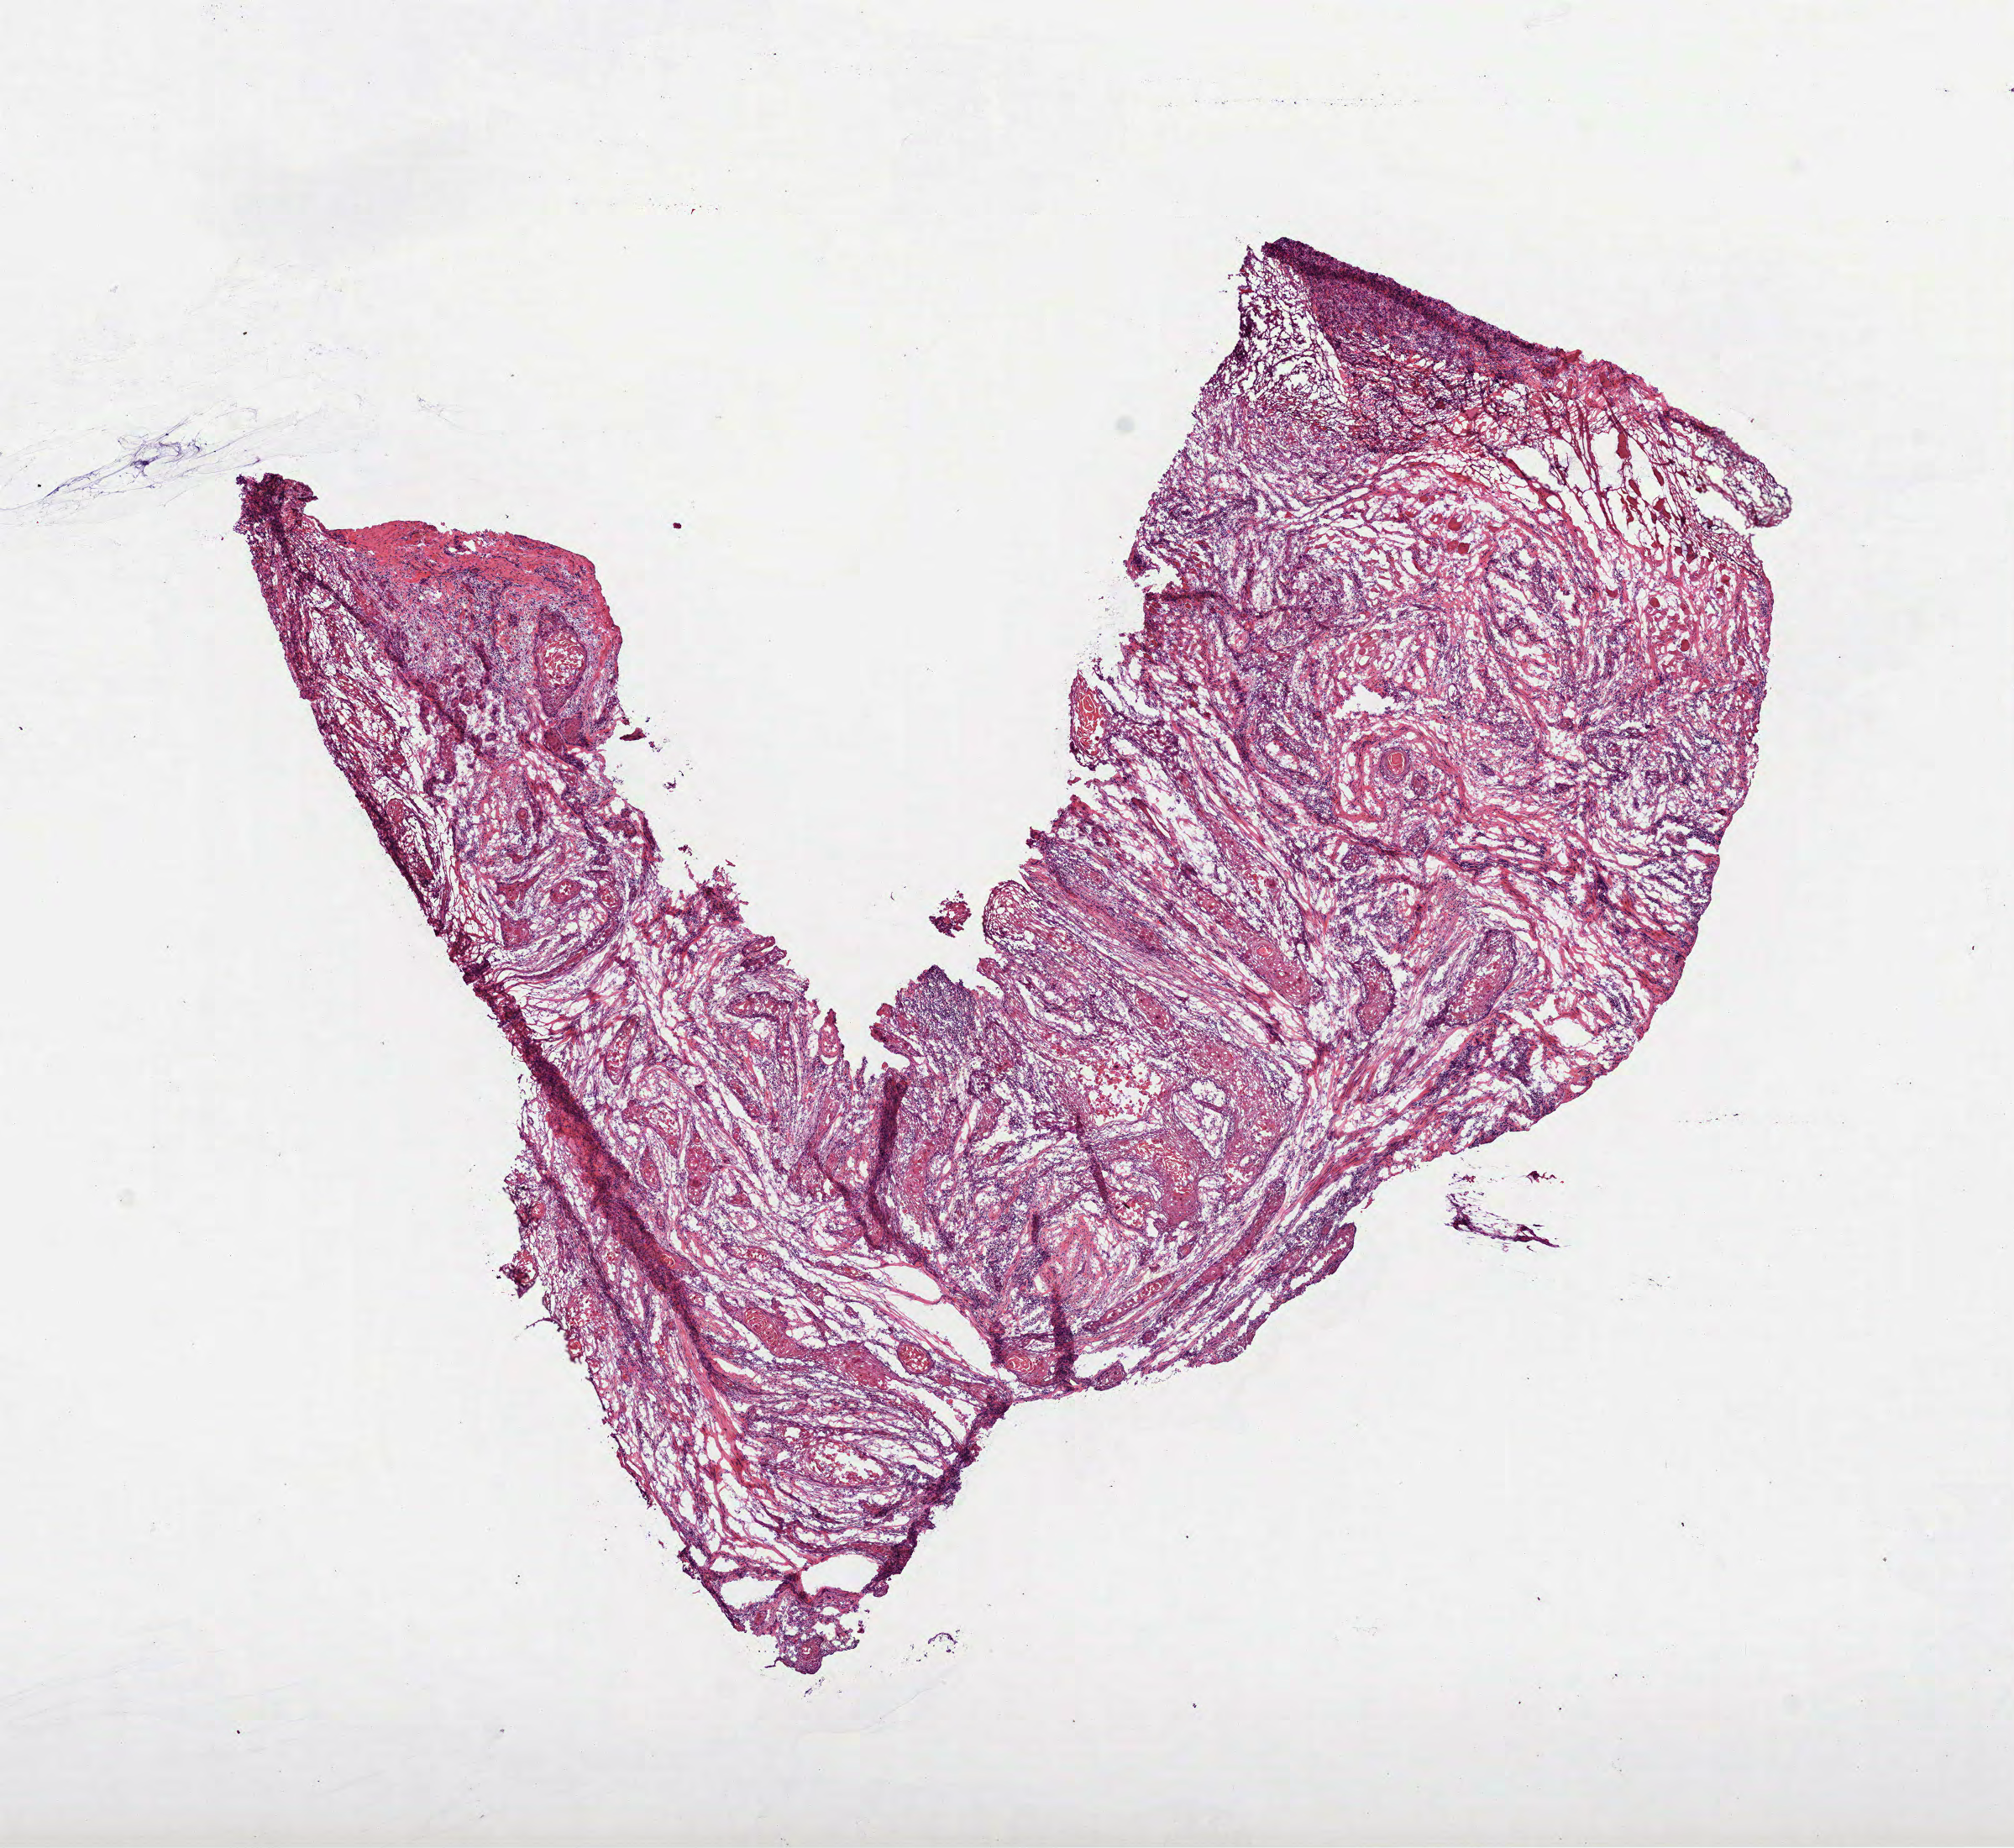
Whole-slide histology image, Hematoxylin and eosin (H&E) stained — whole scanned area (about 9.7 x 8.9 mm, from a 40x scan) shown as a low-resolution overview. Frozen section. Sample: primary tumour, head and neck. Patient: male, age at initial diagnosis 74 years. Histologic grade: G2 (moderately differentiated). Slide review estimates, as recorded: tumour cells 80%, tumour nuclei 61%, normal cells 0%, stromal cells 15%, necrosis 5%. Inflammatory infiltration, as recorded: lymphocyte infiltration 25%, monocyte infiltration 0%, neutrophil infiltration 2%.
• AJCC pathologic stage: III (7th edition)
• diagnosis: Squamous cell carcinoma, NOS